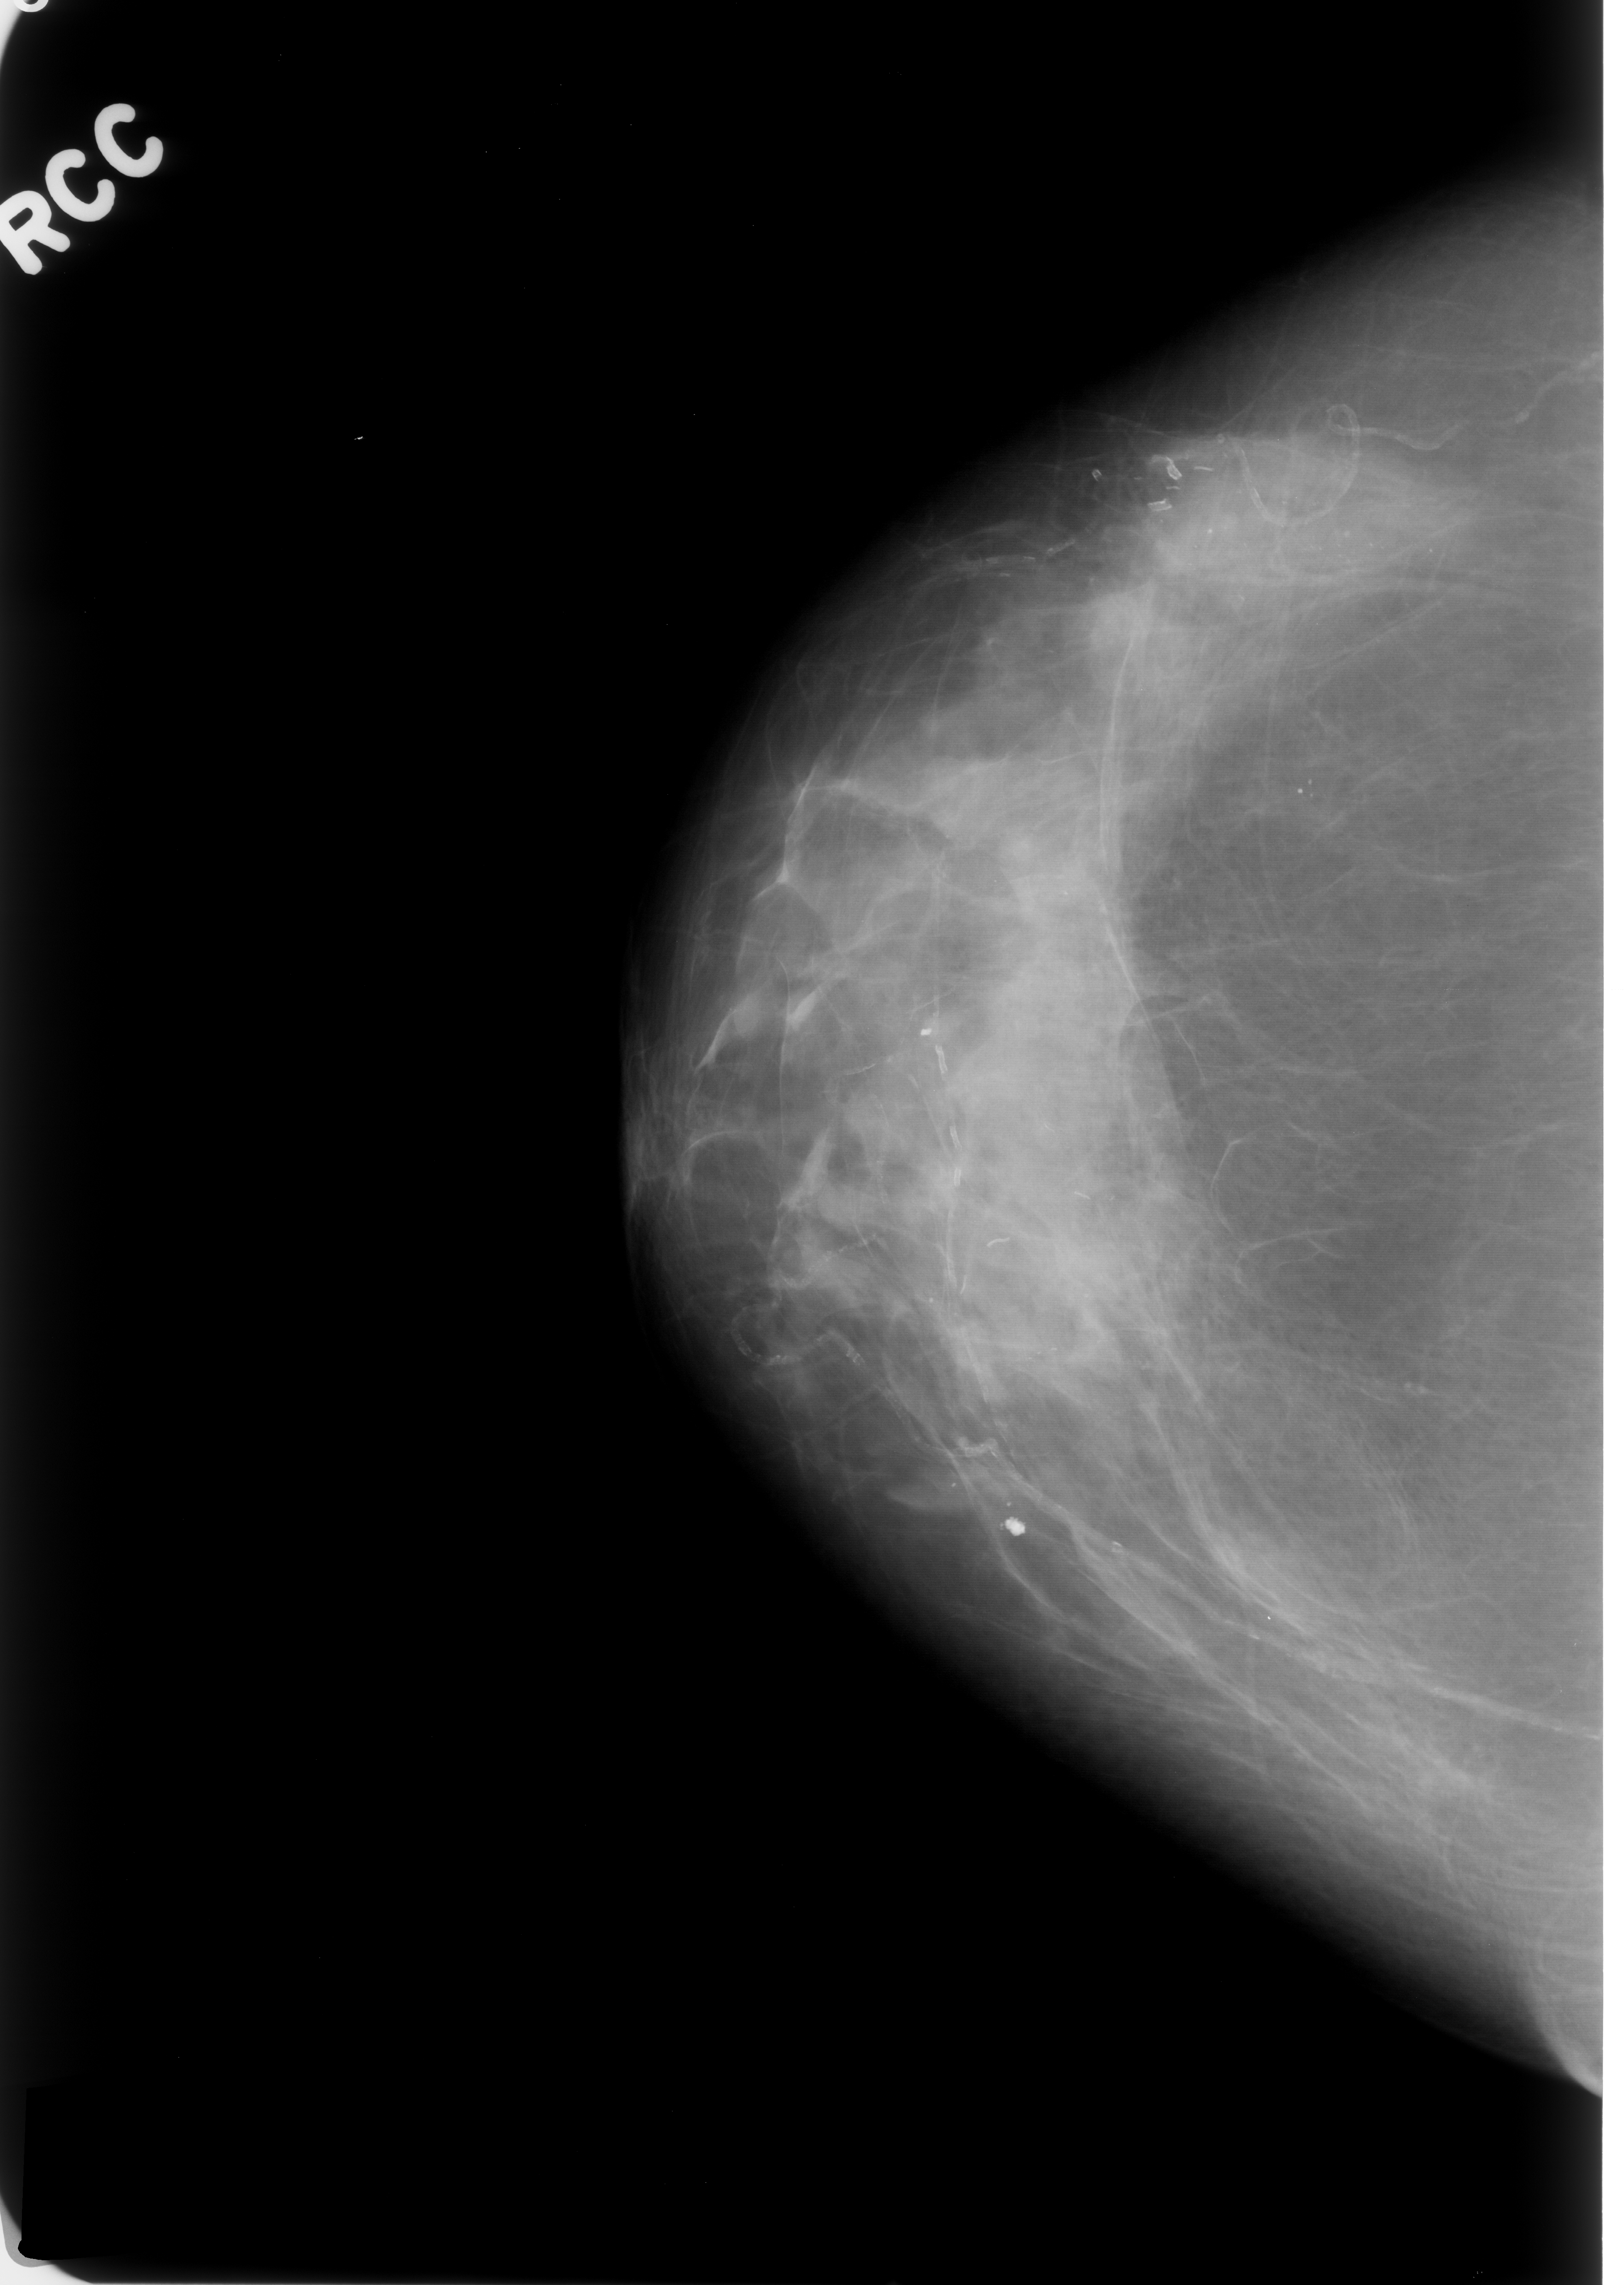
Scanned film-screen mammogram; right breast; CC view; BI-RADS breast density category 2 (scale 1–4); 1624 × 2285 image matrix.
Marked abnormalities (boxes around the expert regions of interest):
- calcifications, morphology punctate, distribution segmental; BI-RADS assessment category 4; subtlety rating 2 on a 1 (subtle) to 5 (obvious) scale; pathology (as recorded): benign: bounding box [x1, y1, x2, y2] px = [1103, 406, 1495, 678]